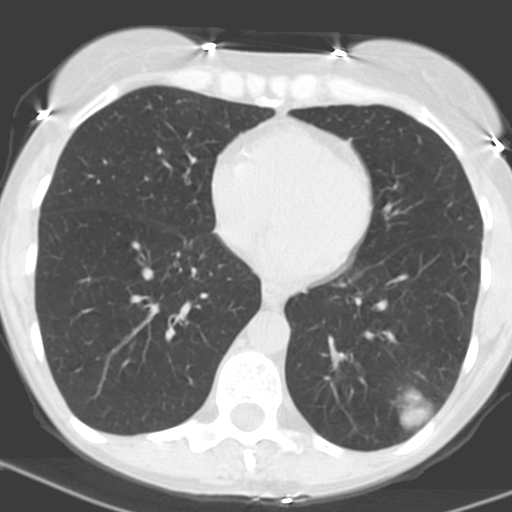
Low-dose screening chest CT, axial slice, baseline annual screen, lung window (W 1500 / L -600 HU), 3.2 mm slice thickness, slice 96 of 156 in the series, 512 × 512 image matrix, field of view 262 × 262 mm. Female participant, aged 56 years at enrolment. Current smoker at enrolment.
Lesion marked by an expert reader, bounding box <369,367,451,440> (left, top, right, bottom; pixels). The exam's reader record, not a measurement of the box and not confirmed to be the same lesion: non-calcified nodule or mass ≥4 mm, left lower lobe, 31 × 23 mm, poorly defined margins, soft tissue attenuation, pre-existing on the prior screen: no.